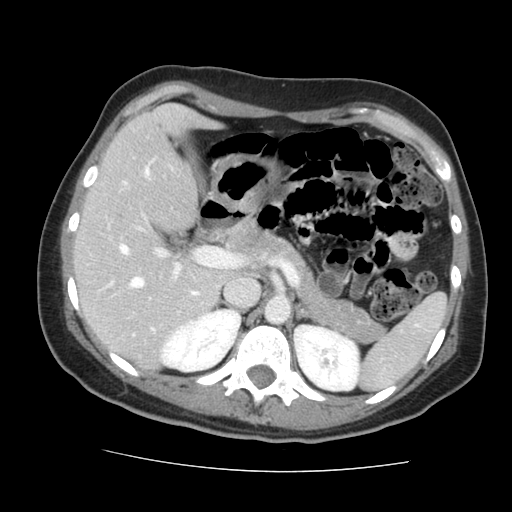
Contrast-enhanced abdominal CT, one axial slice; slice 91 of 144 in the series (ordered by position); 120 kVp; intravenous contrast given; soft-tissue window (W 400 / L 40 HU); 2.5 mm slice thickness; 512 × 512 image matrix. Female patient, age 46 years. Case-level facts recorded for this patient, not image findings: diagnosis: colorectal cancer liver metastases, imaged before liver resection; multiple liver metastases: no; largest metastasis: 2.8 cm; disease in both lobes: no.
Structures marked on this image (expert manual segmentation):
- hepatic veins: box from (x=123, y=168) to (x=197, y=295) px
- liver: (x=78, y=106)–(x=222, y=367)
- planned liver remnant (the part of the liver to remain after resection): (x=78, y=106)–(x=222, y=367)
- portal vein (with intrahepatic branches): (x=111, y=226)–(x=226, y=330)